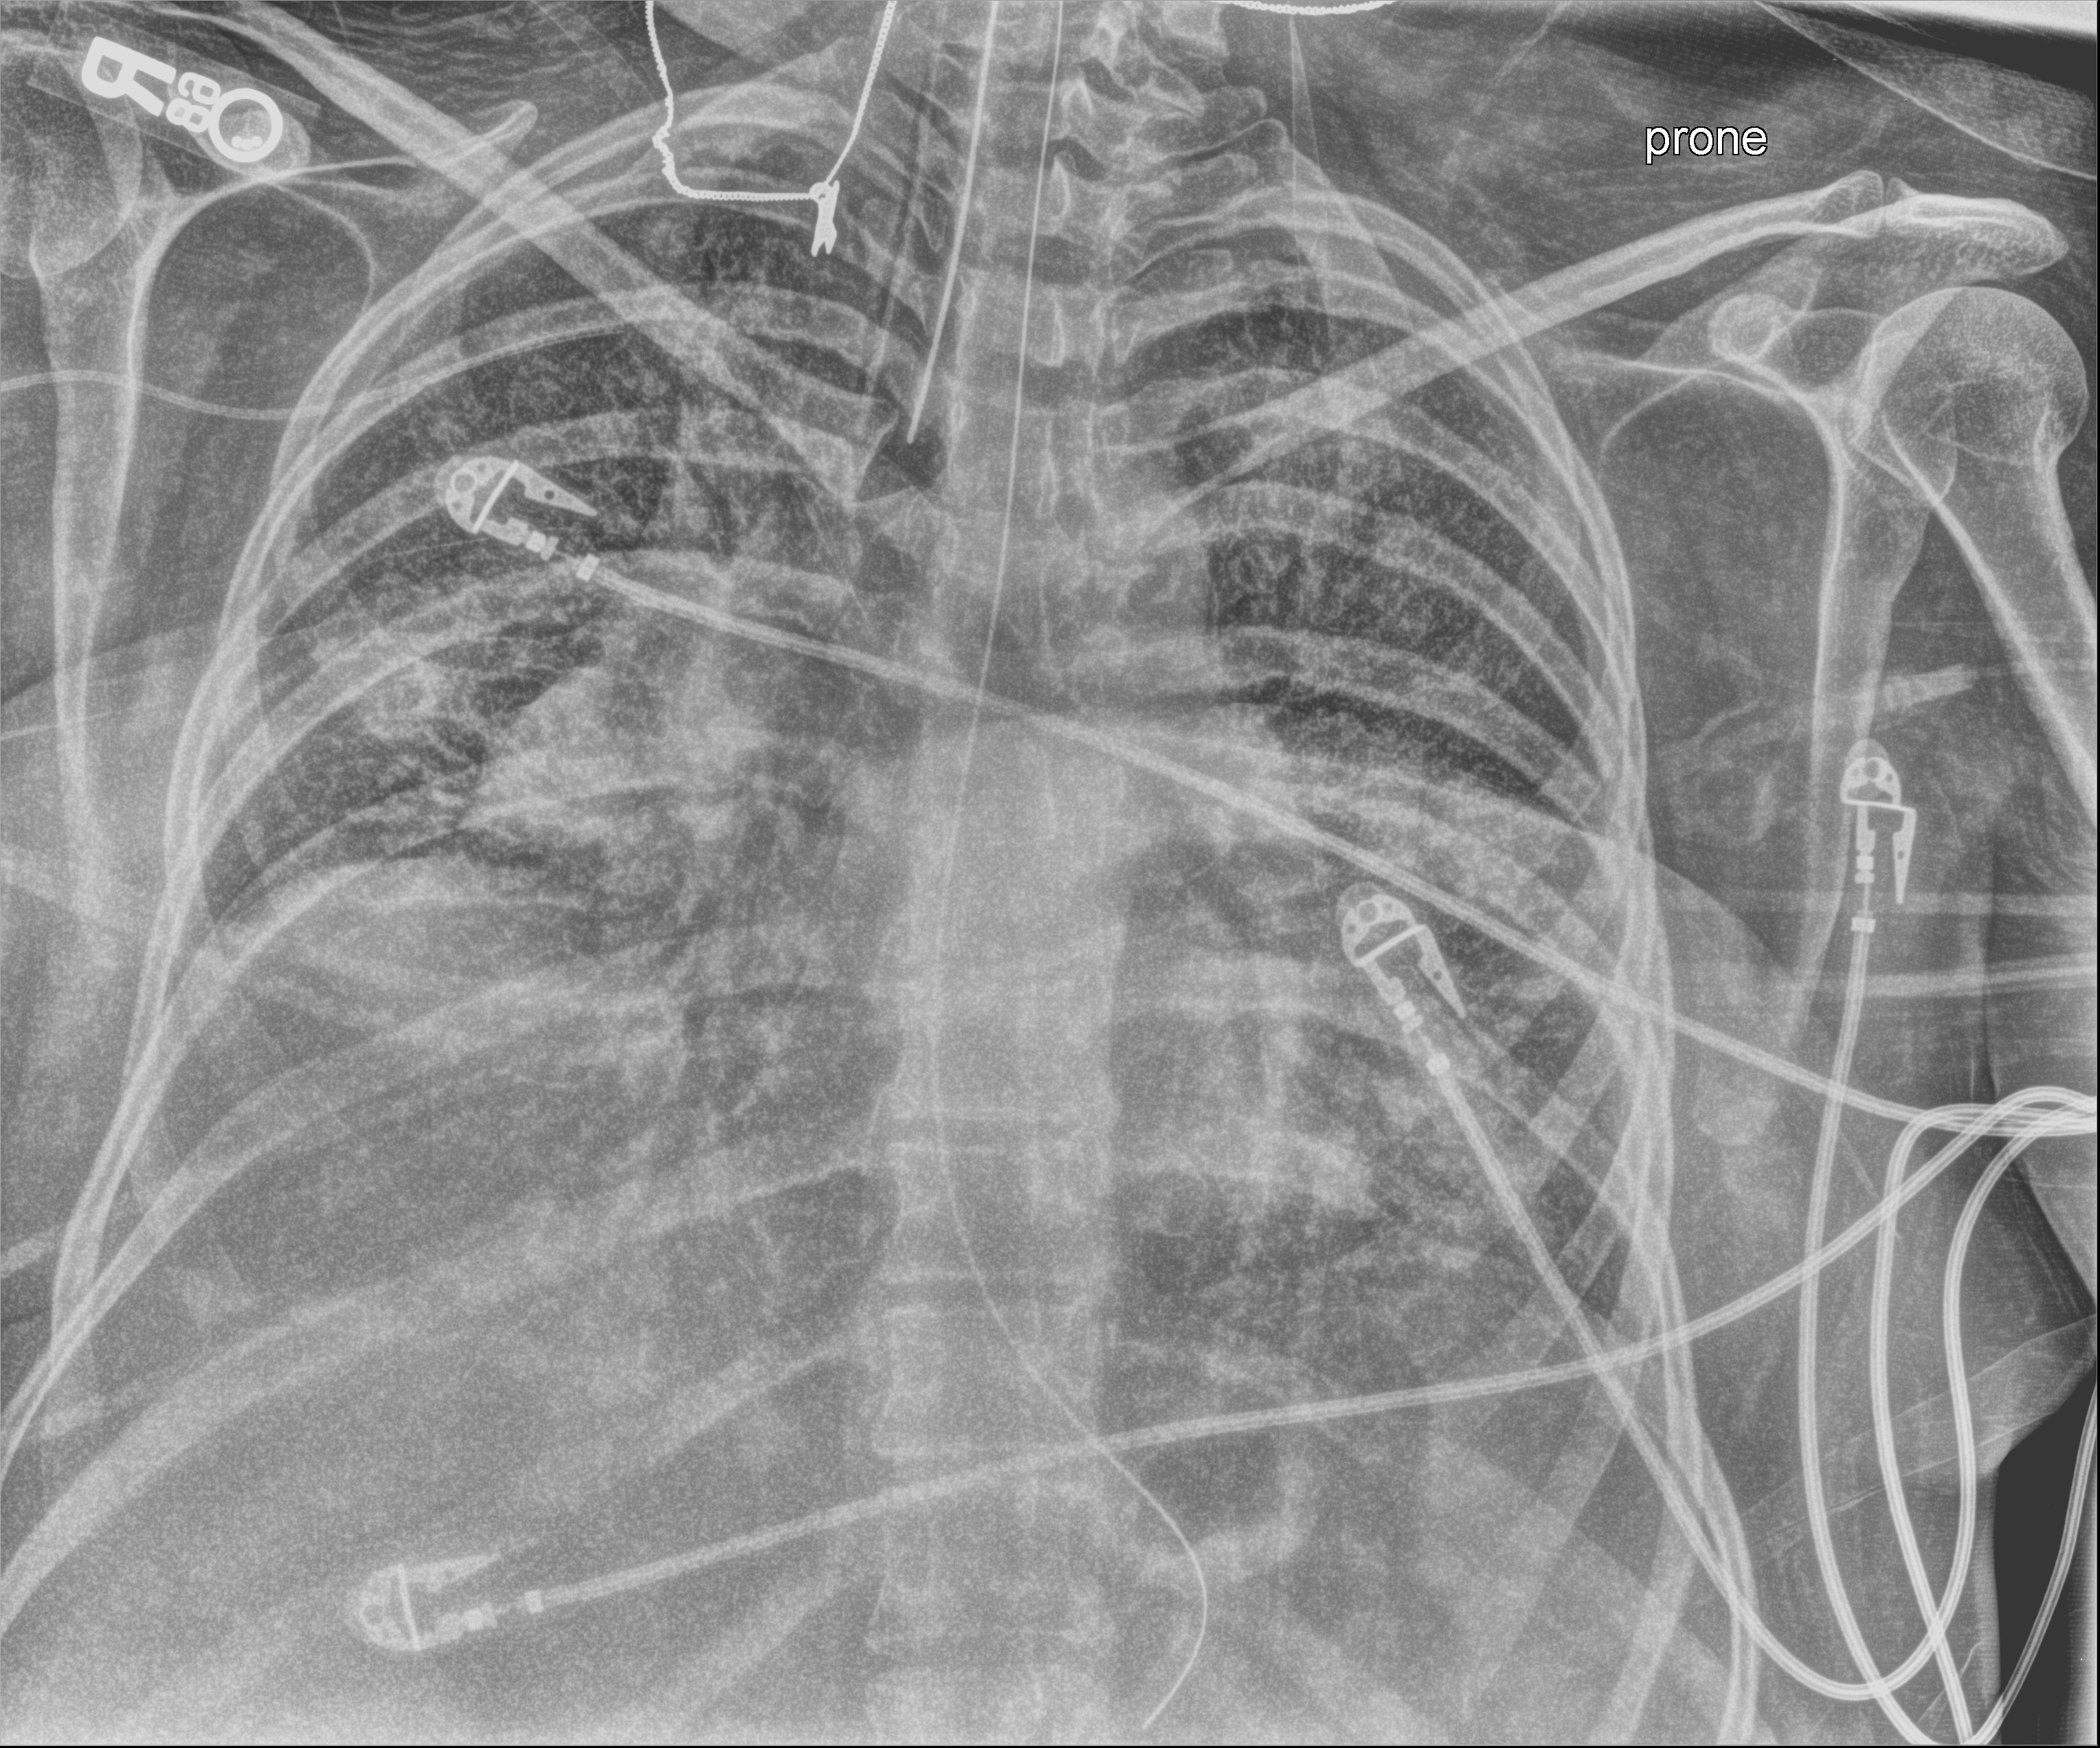
Chest X-ray (portable). Female patient hospitalised with COVID-19, age 18–59 years.
From the hospital-stay record, not from the radiograph (when in the stay this image was taken is not recorded): mechanically ventilated during this hospital stay: yes.